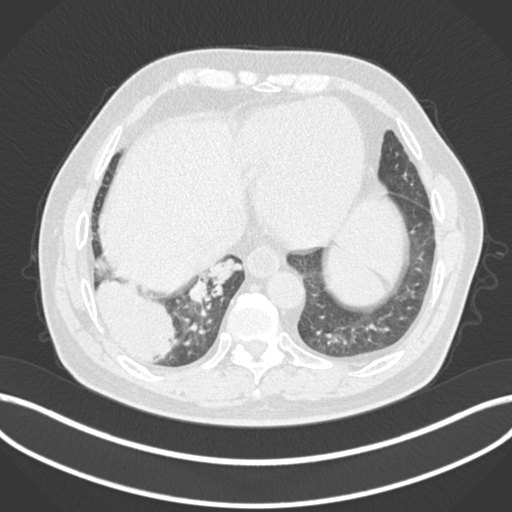
Chest CT, one axial slice; reconstruction kernel B30f; 120 kVp; lung window (W 1500 / L -600 HU); 1 mm slice thickness; 512 × 512 image matrix, field of view 400 × 400 mm. Patient: male, 59 years.
Structures marked on this image (bounding box drawn by a radiologist):
- lung tumour (recorded histology: adenocarcinoma): bounding box <92,273,180,365> (left, top, right, bottom; pixels)